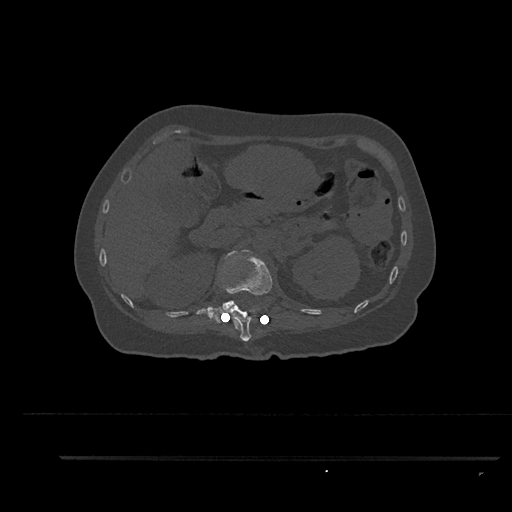
CT including the spine, one axial slice. Slice 241 of 797 in the series (ordered by position). 120 kVp. Bone window (W 1800 / L 400 HU). 512 × 512 image matrix, field of view 408 × 408 mm. Patient: female, 44 years. From the clinical record (not read from this slice): primary cancer: renal; vertebrae with lytic lesions (as recorded): L1.
Annotated regions visible in this slice (semi-automatically segmented with operator editing):
- L1 vertebra: box from (x=208, y=249) to (x=253, y=317) px
- T12 vertebra: (x=206, y=251)–(x=273, y=342)